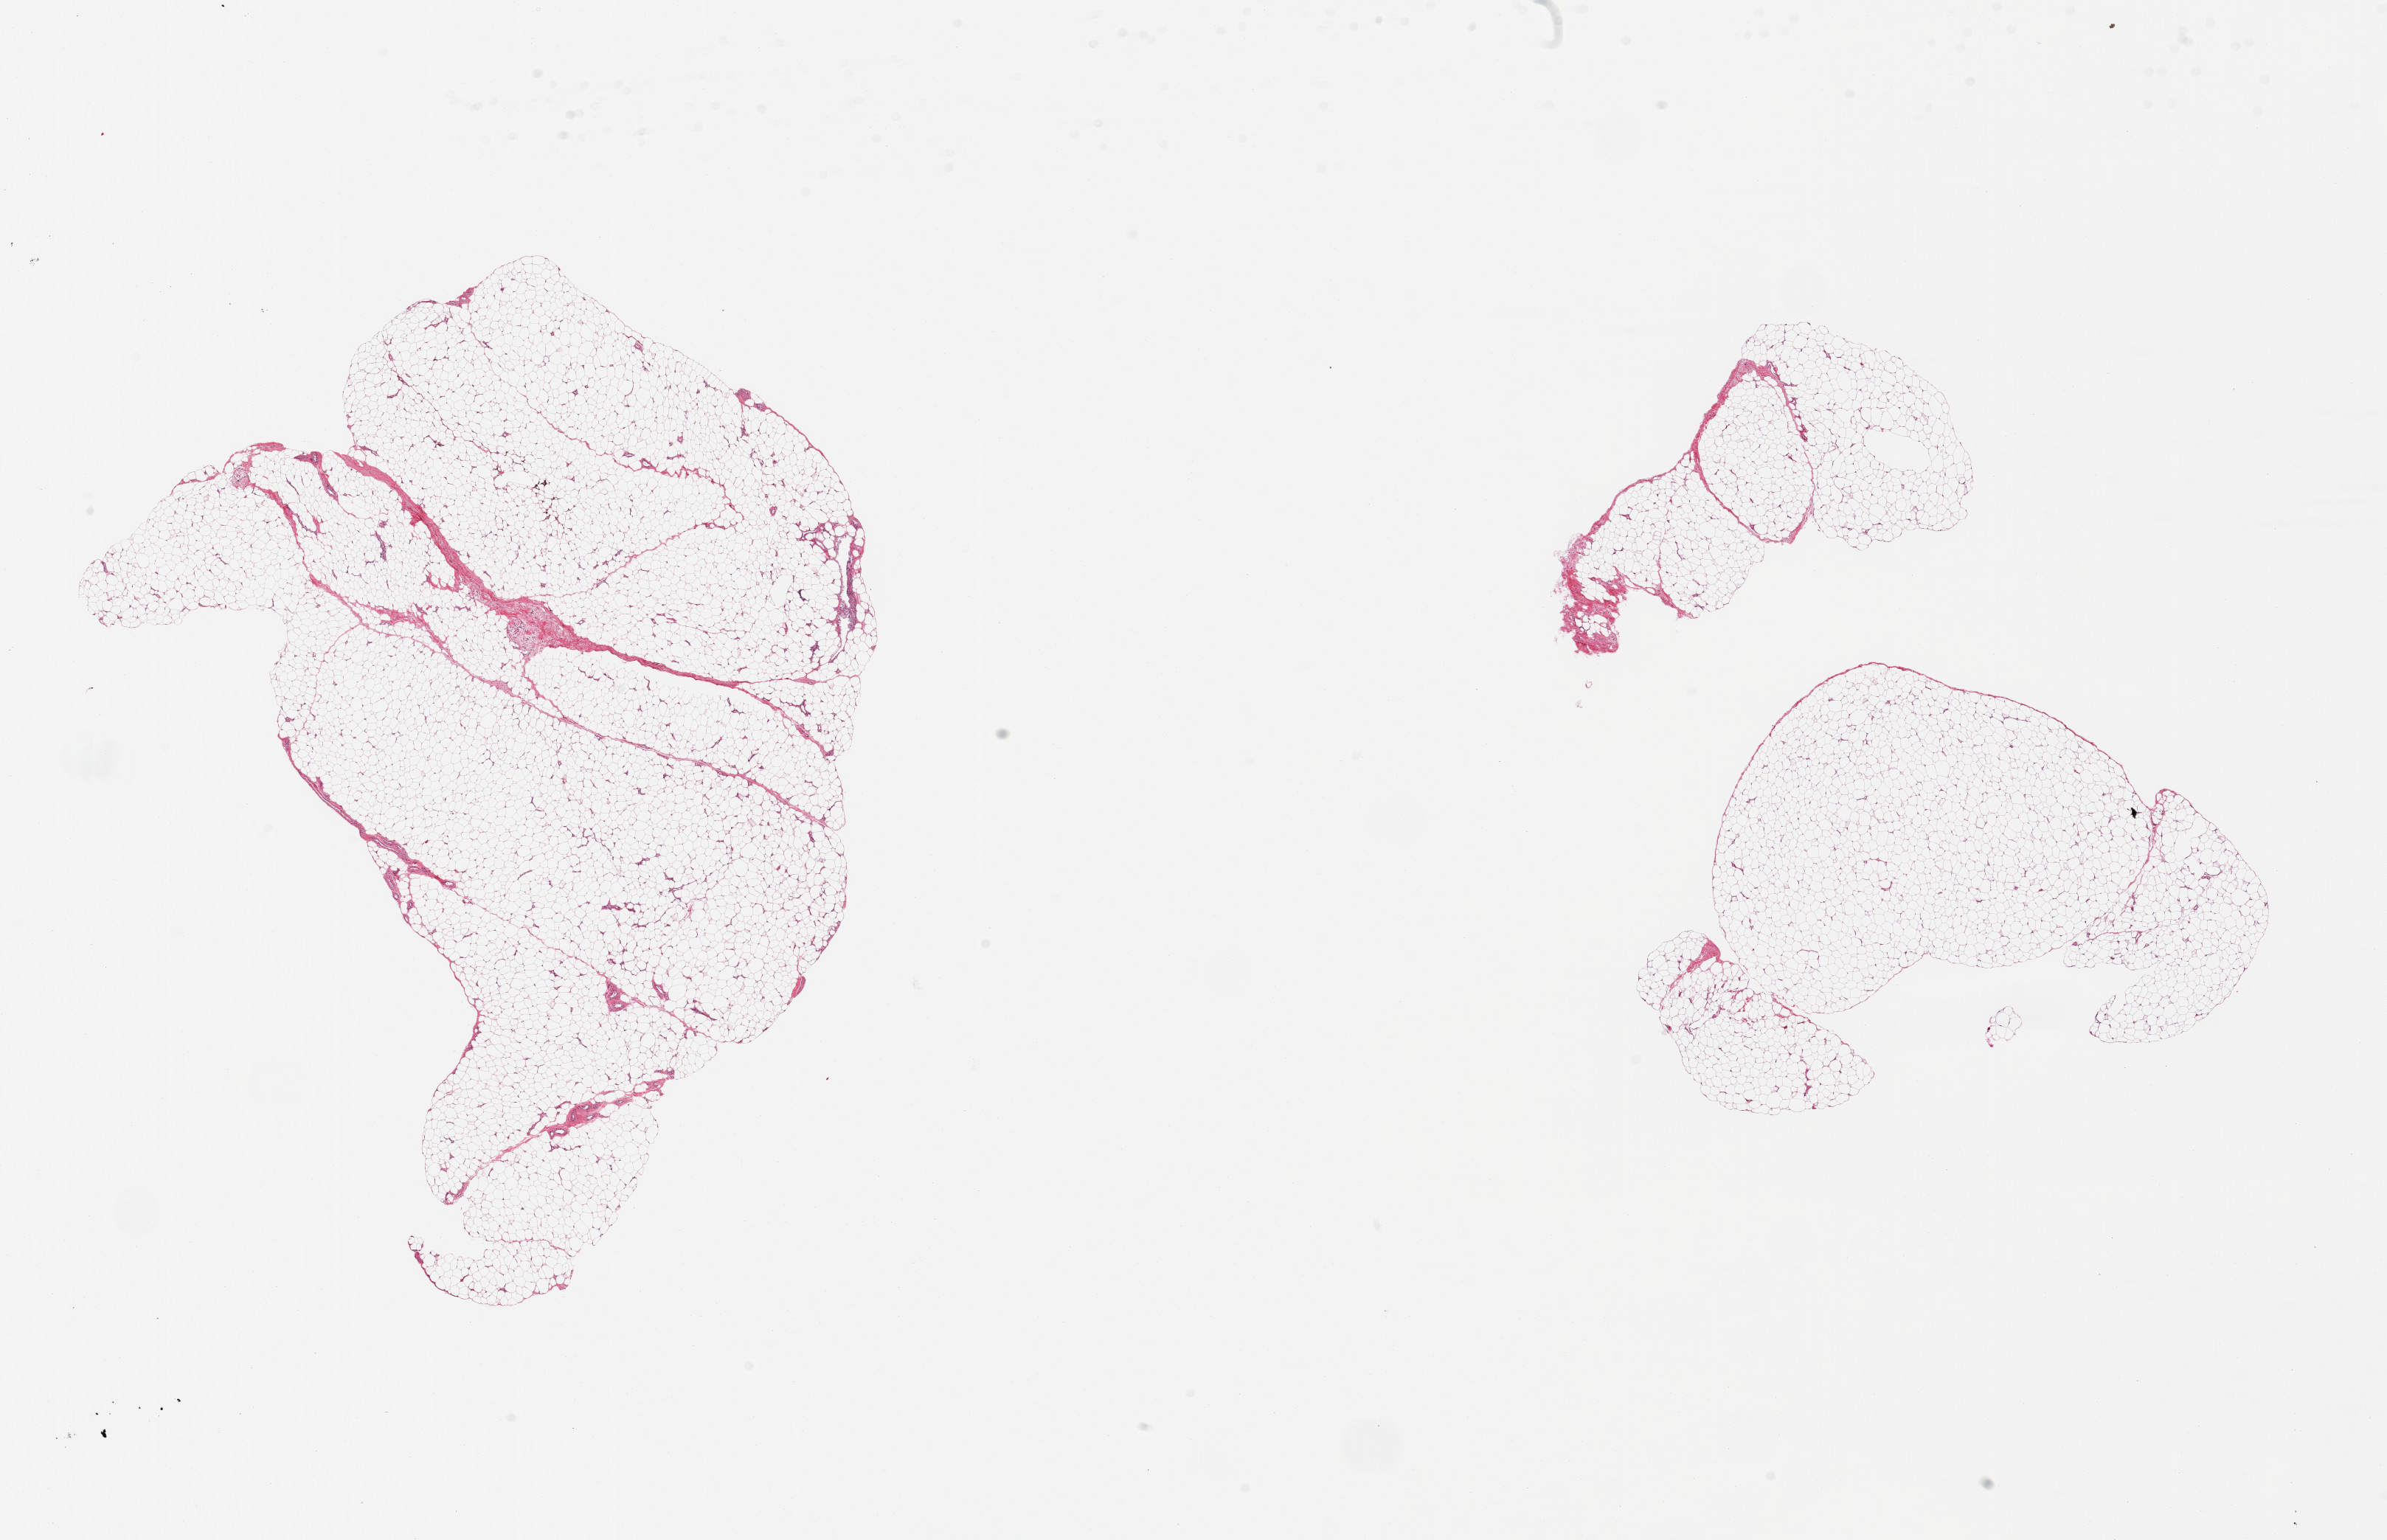
Digitized hematoxylin and eosin (H&E)-stained section, brightfield, shown as a low-resolution overview of the whole scanned area (about 25.6 x 16.5 mm, slide scanned at 20x), PAXgene-fixed paraffin-embedded (PFPE) section, target tissue: adipose tissue, tissue donor sample. Donor sex: female.
Reviewer comment on this tissue sample: 2 pieces; <5% fibrous content.